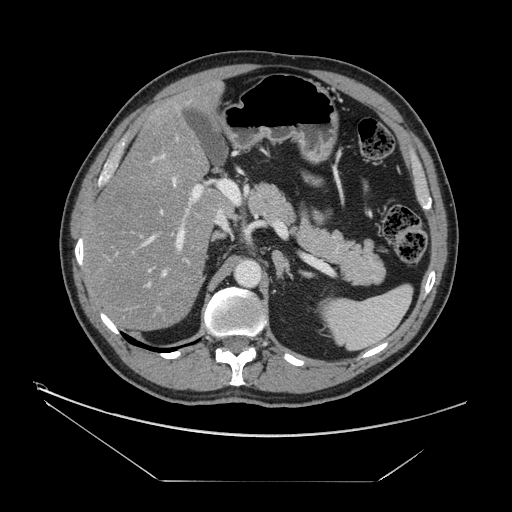
Contrast-enhanced abdominal CT, one axial slice. Slice 87 of 161 in the series (ordered by position). Reconstruction kernel STANDARD. 120 kVp. Intravenous contrast given. Soft-tissue window (W 400 / L 40 HU). 2.5 mm slice thickness. 512 × 512 image matrix, field of view 440 × 440 mm. Male patient, age 65 years. Case-level facts recorded for this patient, not image findings: diagnosis: colorectal cancer liver metastases, imaged before liver resection; multiple liver metastases: yes.
Outlined on this slice (expert manual segmentation):
- hepatic veins: bounding box [x1, y1, x2, y2] px = [140, 177, 177, 288]
- liver: [85, 86, 228, 330]
- planned liver remnant (the part of the liver to remain after resection): [87, 85, 226, 330]
- portal vein (with intrahepatic branches): [111, 154, 221, 320]